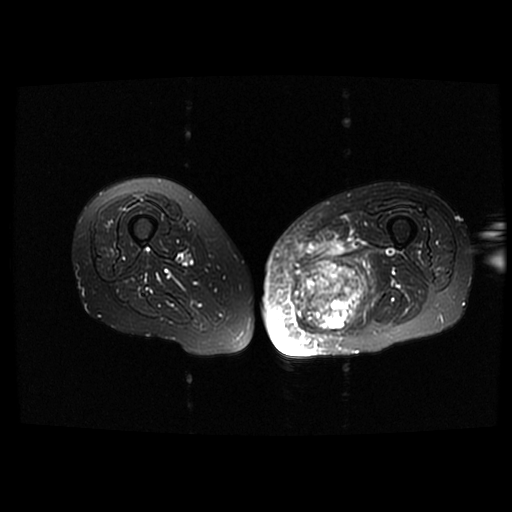
MRI of an extremity soft-tissue mass, one axial slice; position 35 of 42 along the scan axis; T2-weighted fat-saturated; 512 × 512 image matrix, field of view 420 × 420 mm. Female patient. Case-level facts recorded for this patient, not image findings: histological type: pleomorphic leiomyosarcoma; grade: high; site of the primary tumour: left thigh.
Structures marked on this image (manually delineated by an expert):
- gross tumour volume including surrounding oedema: bounding box [x1, y1, x2, y2] px = [293, 239, 375, 335]
- gross tumour volume (mass): [293, 260, 365, 335]